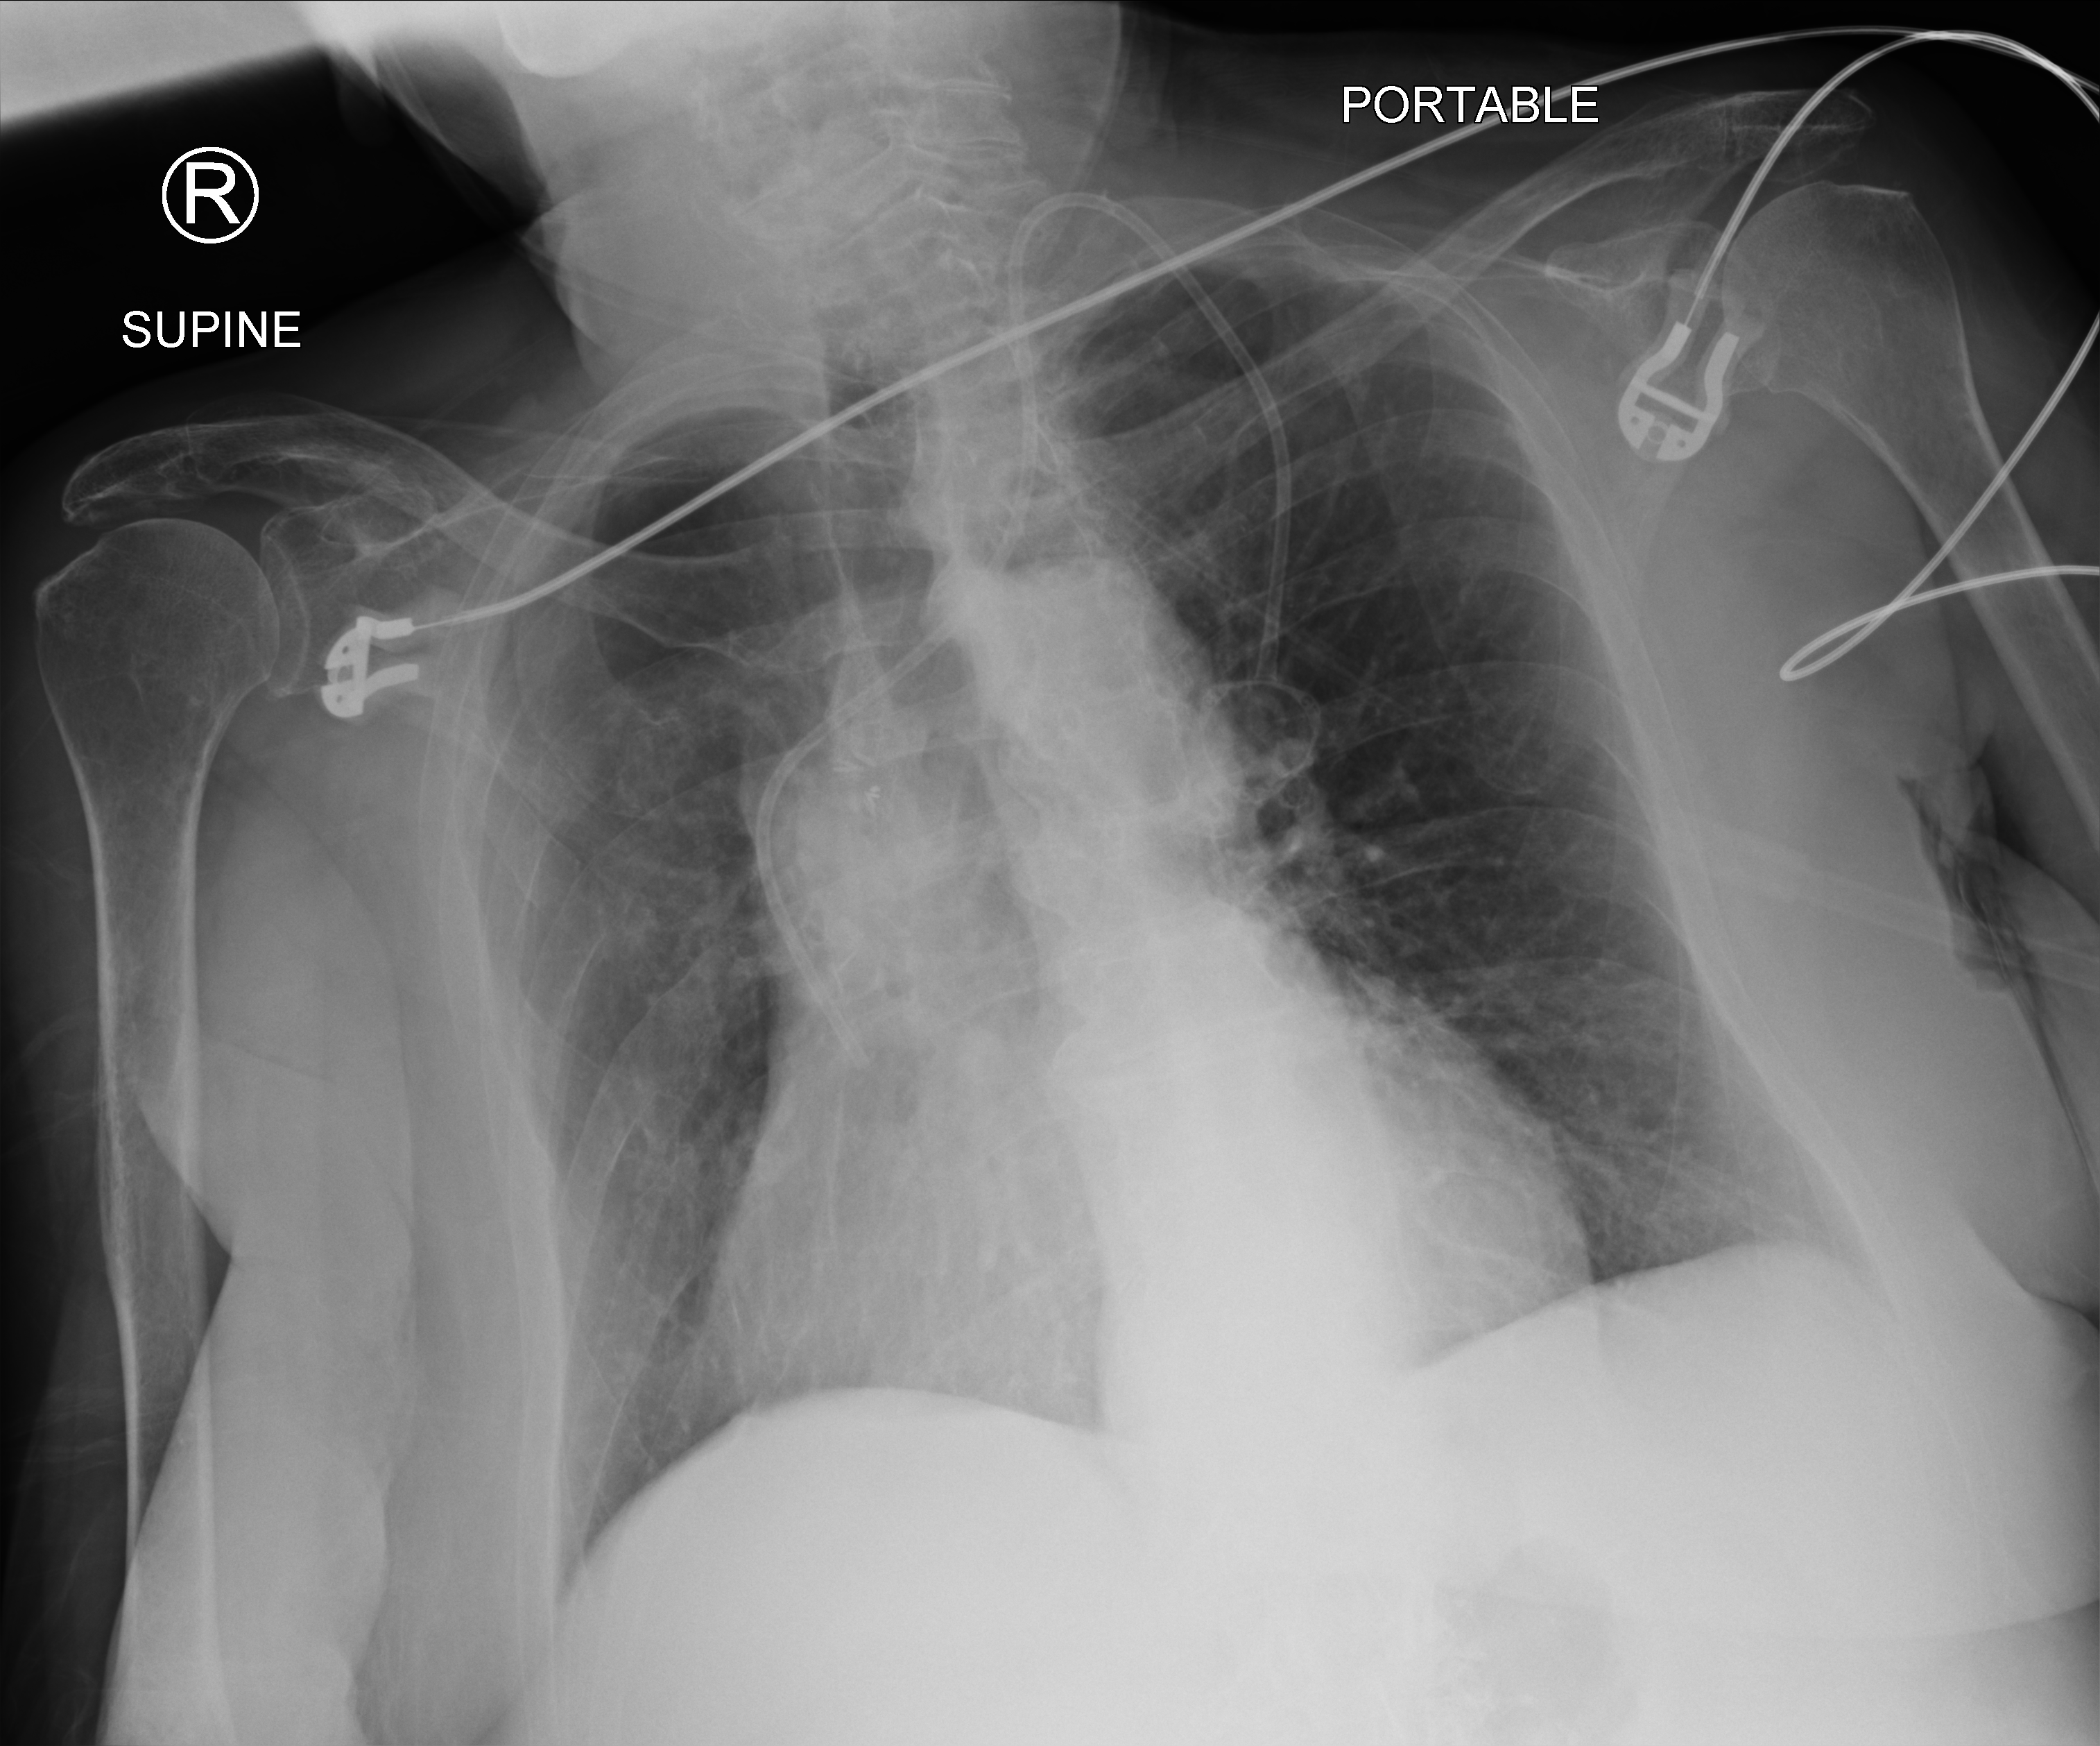
Chest X-ray (portable); anteroposterior (AP) projection. Female patient hospitalised with COVID-19, age 75–90 years.
Admission-level facts for this patient (not findings on this image; timing relative to this image not recorded): mechanically ventilated during this hospital stay: no.